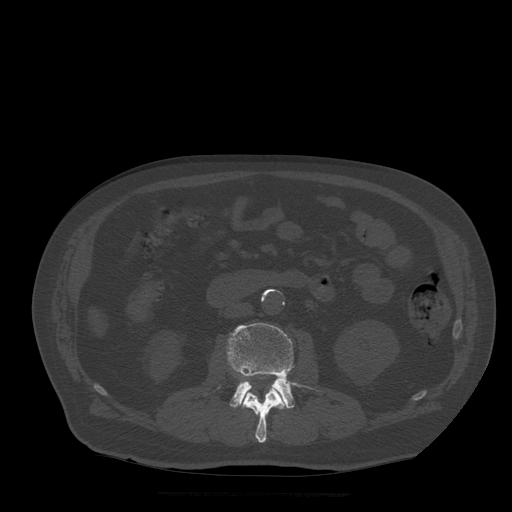
CT including the spine, one axial slice; slice 154 of 522 in the series (ordered by position); bone window (W 1800 / L 400 HU); 512 × 512 image matrix, field of view 420 × 420 mm. Patient age 72 years. From the clinical record (not read from this slice): primary cancer: prostate.
Outlined on this slice (semi-automatically segmented with operator editing):
- L2 vertebra: bounding box [x1, y1, x2, y2] px = [243, 378, 286, 443]
- L3 vertebra: [227, 323, 311, 409]